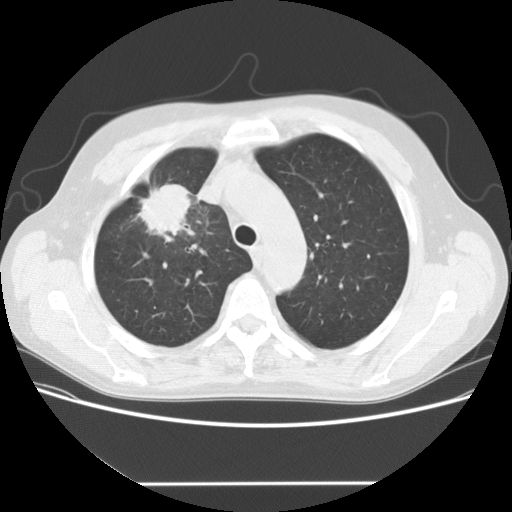
Axial slice from a low-dose chest CT screening exam. First (baseline) screen. Lung window (W 1500 / L -600 HU). 2.5 mm slice thickness. 512 × 512 image matrix, field of view 360 × 360 mm. Male, age 56 years at enrolment. Current smoker at enrolment.
Expert reader's lesion annotation, bounding box <128,173,212,244> (left, top, right, bottom; pixels). The screening reader recorded 2 non-calcified nodules or masses ≥4 mm on this exam (right upper lobe, right middle lobe); which of them this box marks is not recorded. Participant outcome: lung cancer diagnosed 120 days after this screen — adenocarcinoma, NOS, right upper lobe, stage IIIA (AJCC 6th edition), 34 mm at pathology.